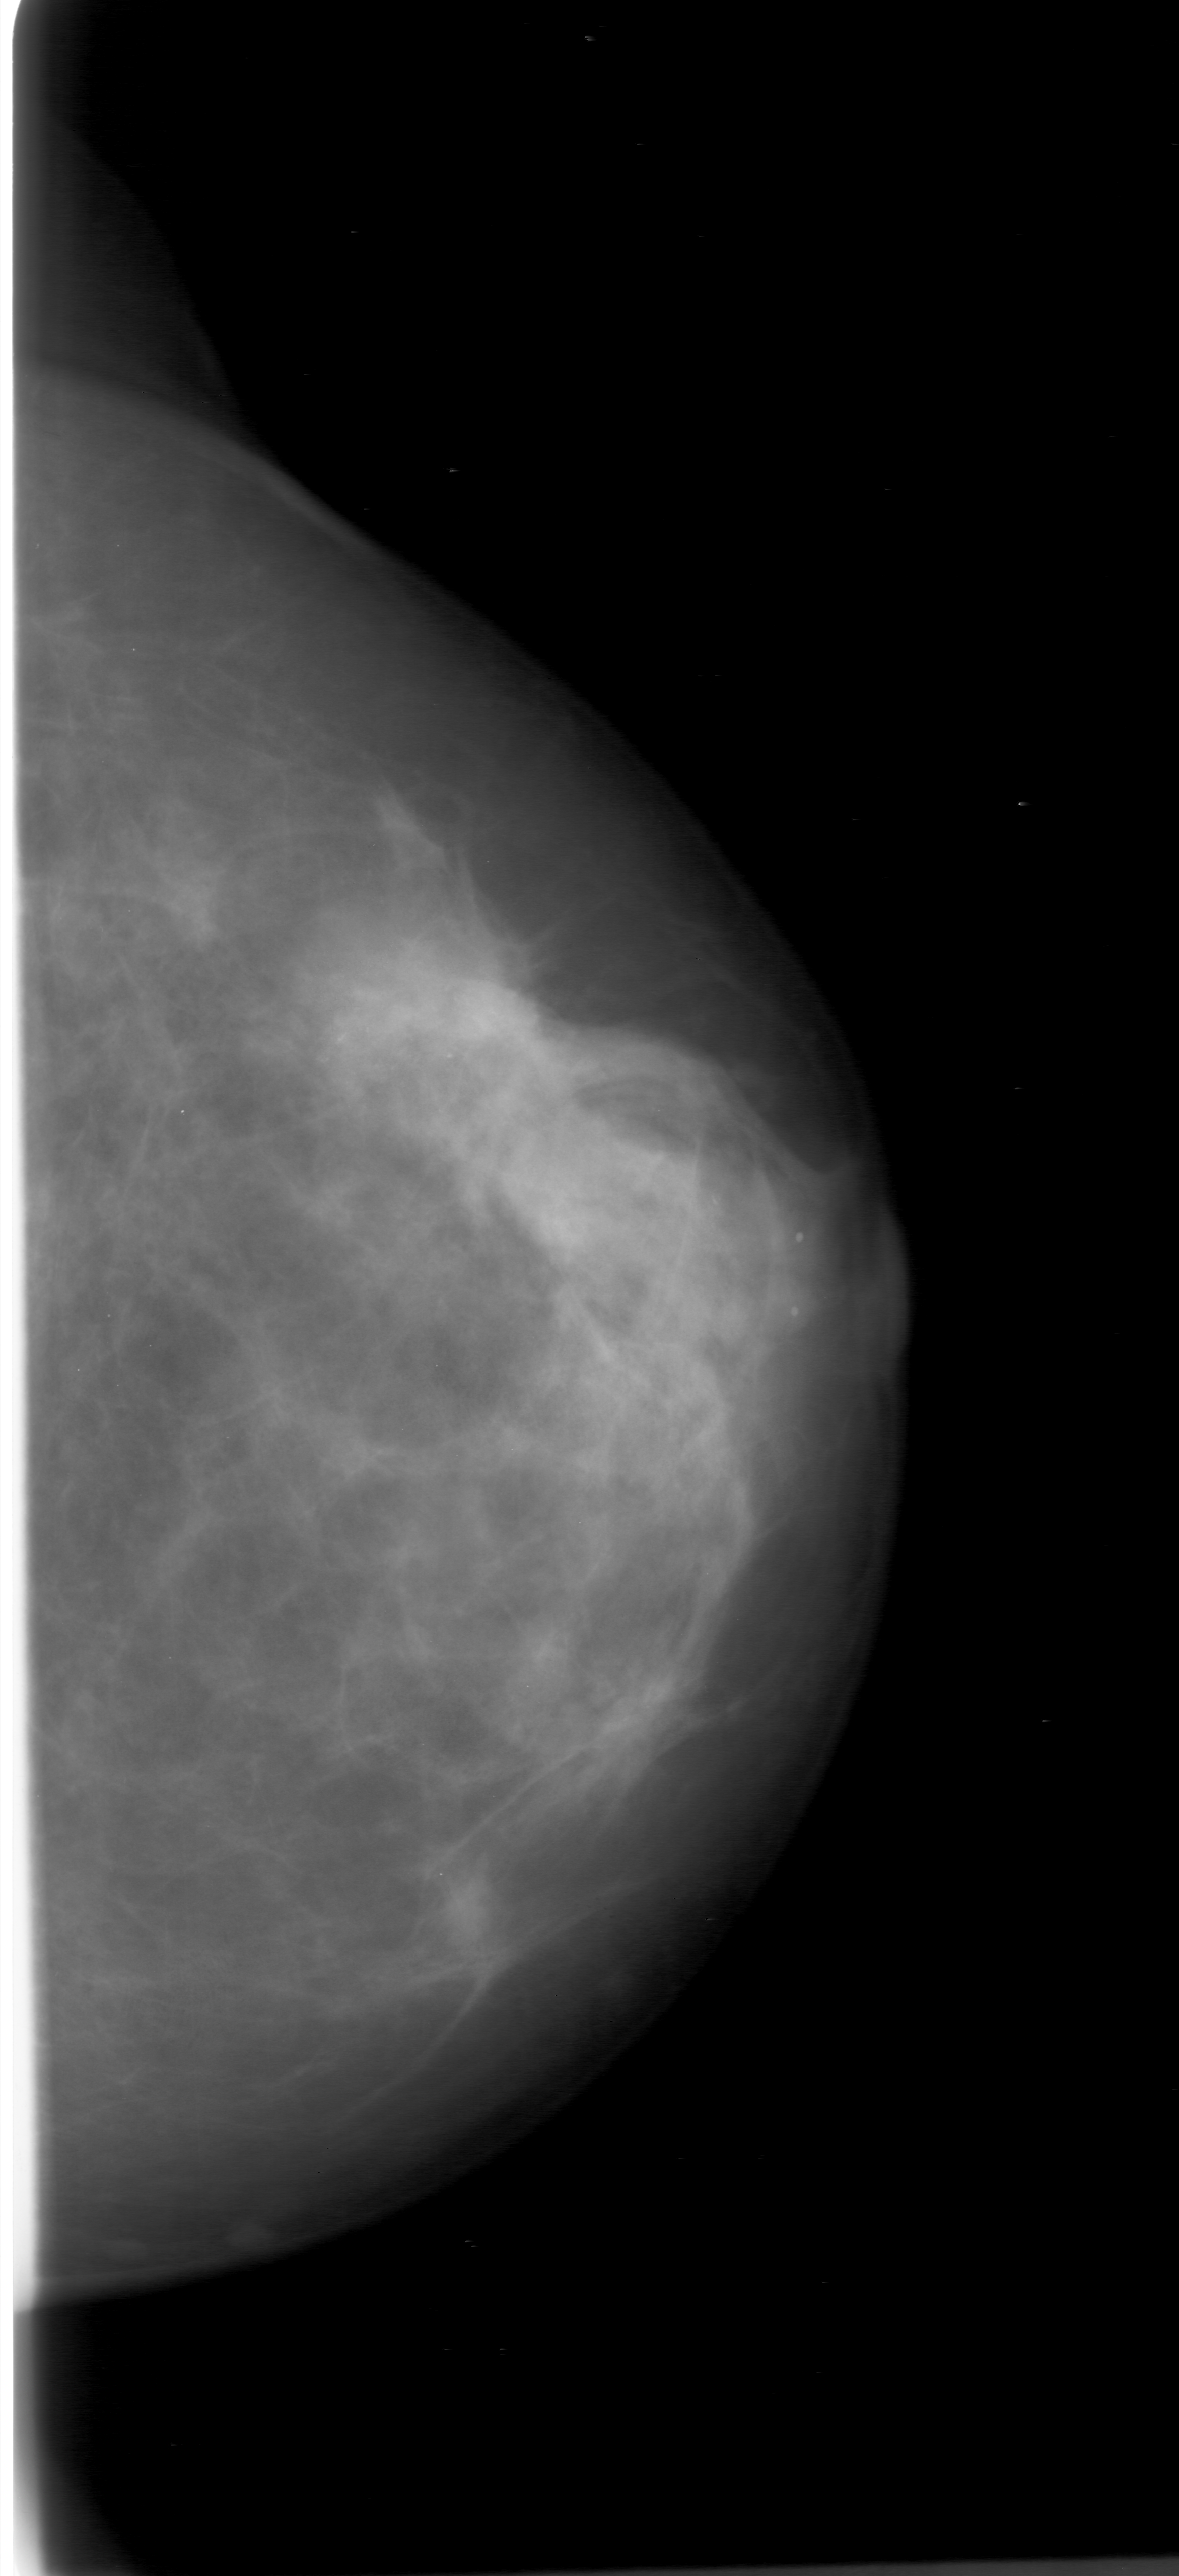
Scanned film-screen mammogram; left breast; craniocaudal (CC) view; breast composition: scattered fibroglandular densities (BI-RADS density category 2 of 4); 1179 × 2576 image matrix.
Marked abnormalities (boxes around the expert regions of interest):
- calcifications, morphology amorphous, distribution segmental; BI-RADS assessment category 4; pathology result (as recorded, not read from the image): malignant: bounding box <190,841,854,1391> (left, top, right, bottom; pixels)